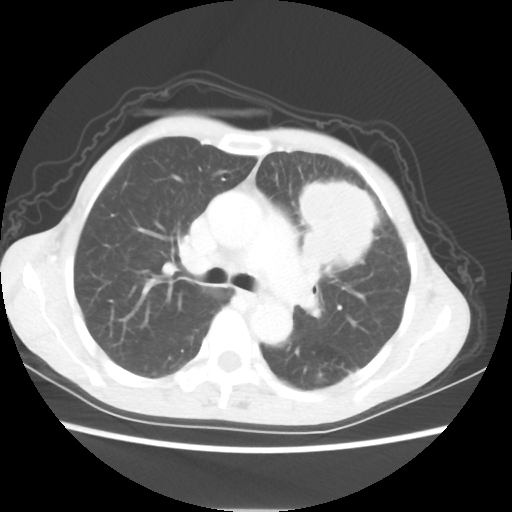
Chest CT, one axial slice. Position 38 of 56 along the scan axis. Reconstruction kernel STANDARD. 80 kVp. Lung window (W 1500 / L -600 HU). 512 × 512 image matrix. Female patient, age 60 years. From the clinical record (not read from this slice): clinical TNM (as recorded): T4 N1 M0.
Structures marked on this image (rectangle marked by the reading radiologist):
- lung tumour (recorded histology: adenocarcinoma): bounding box (x1, y1, x2, y2) in pixels: (288, 173, 380, 276)